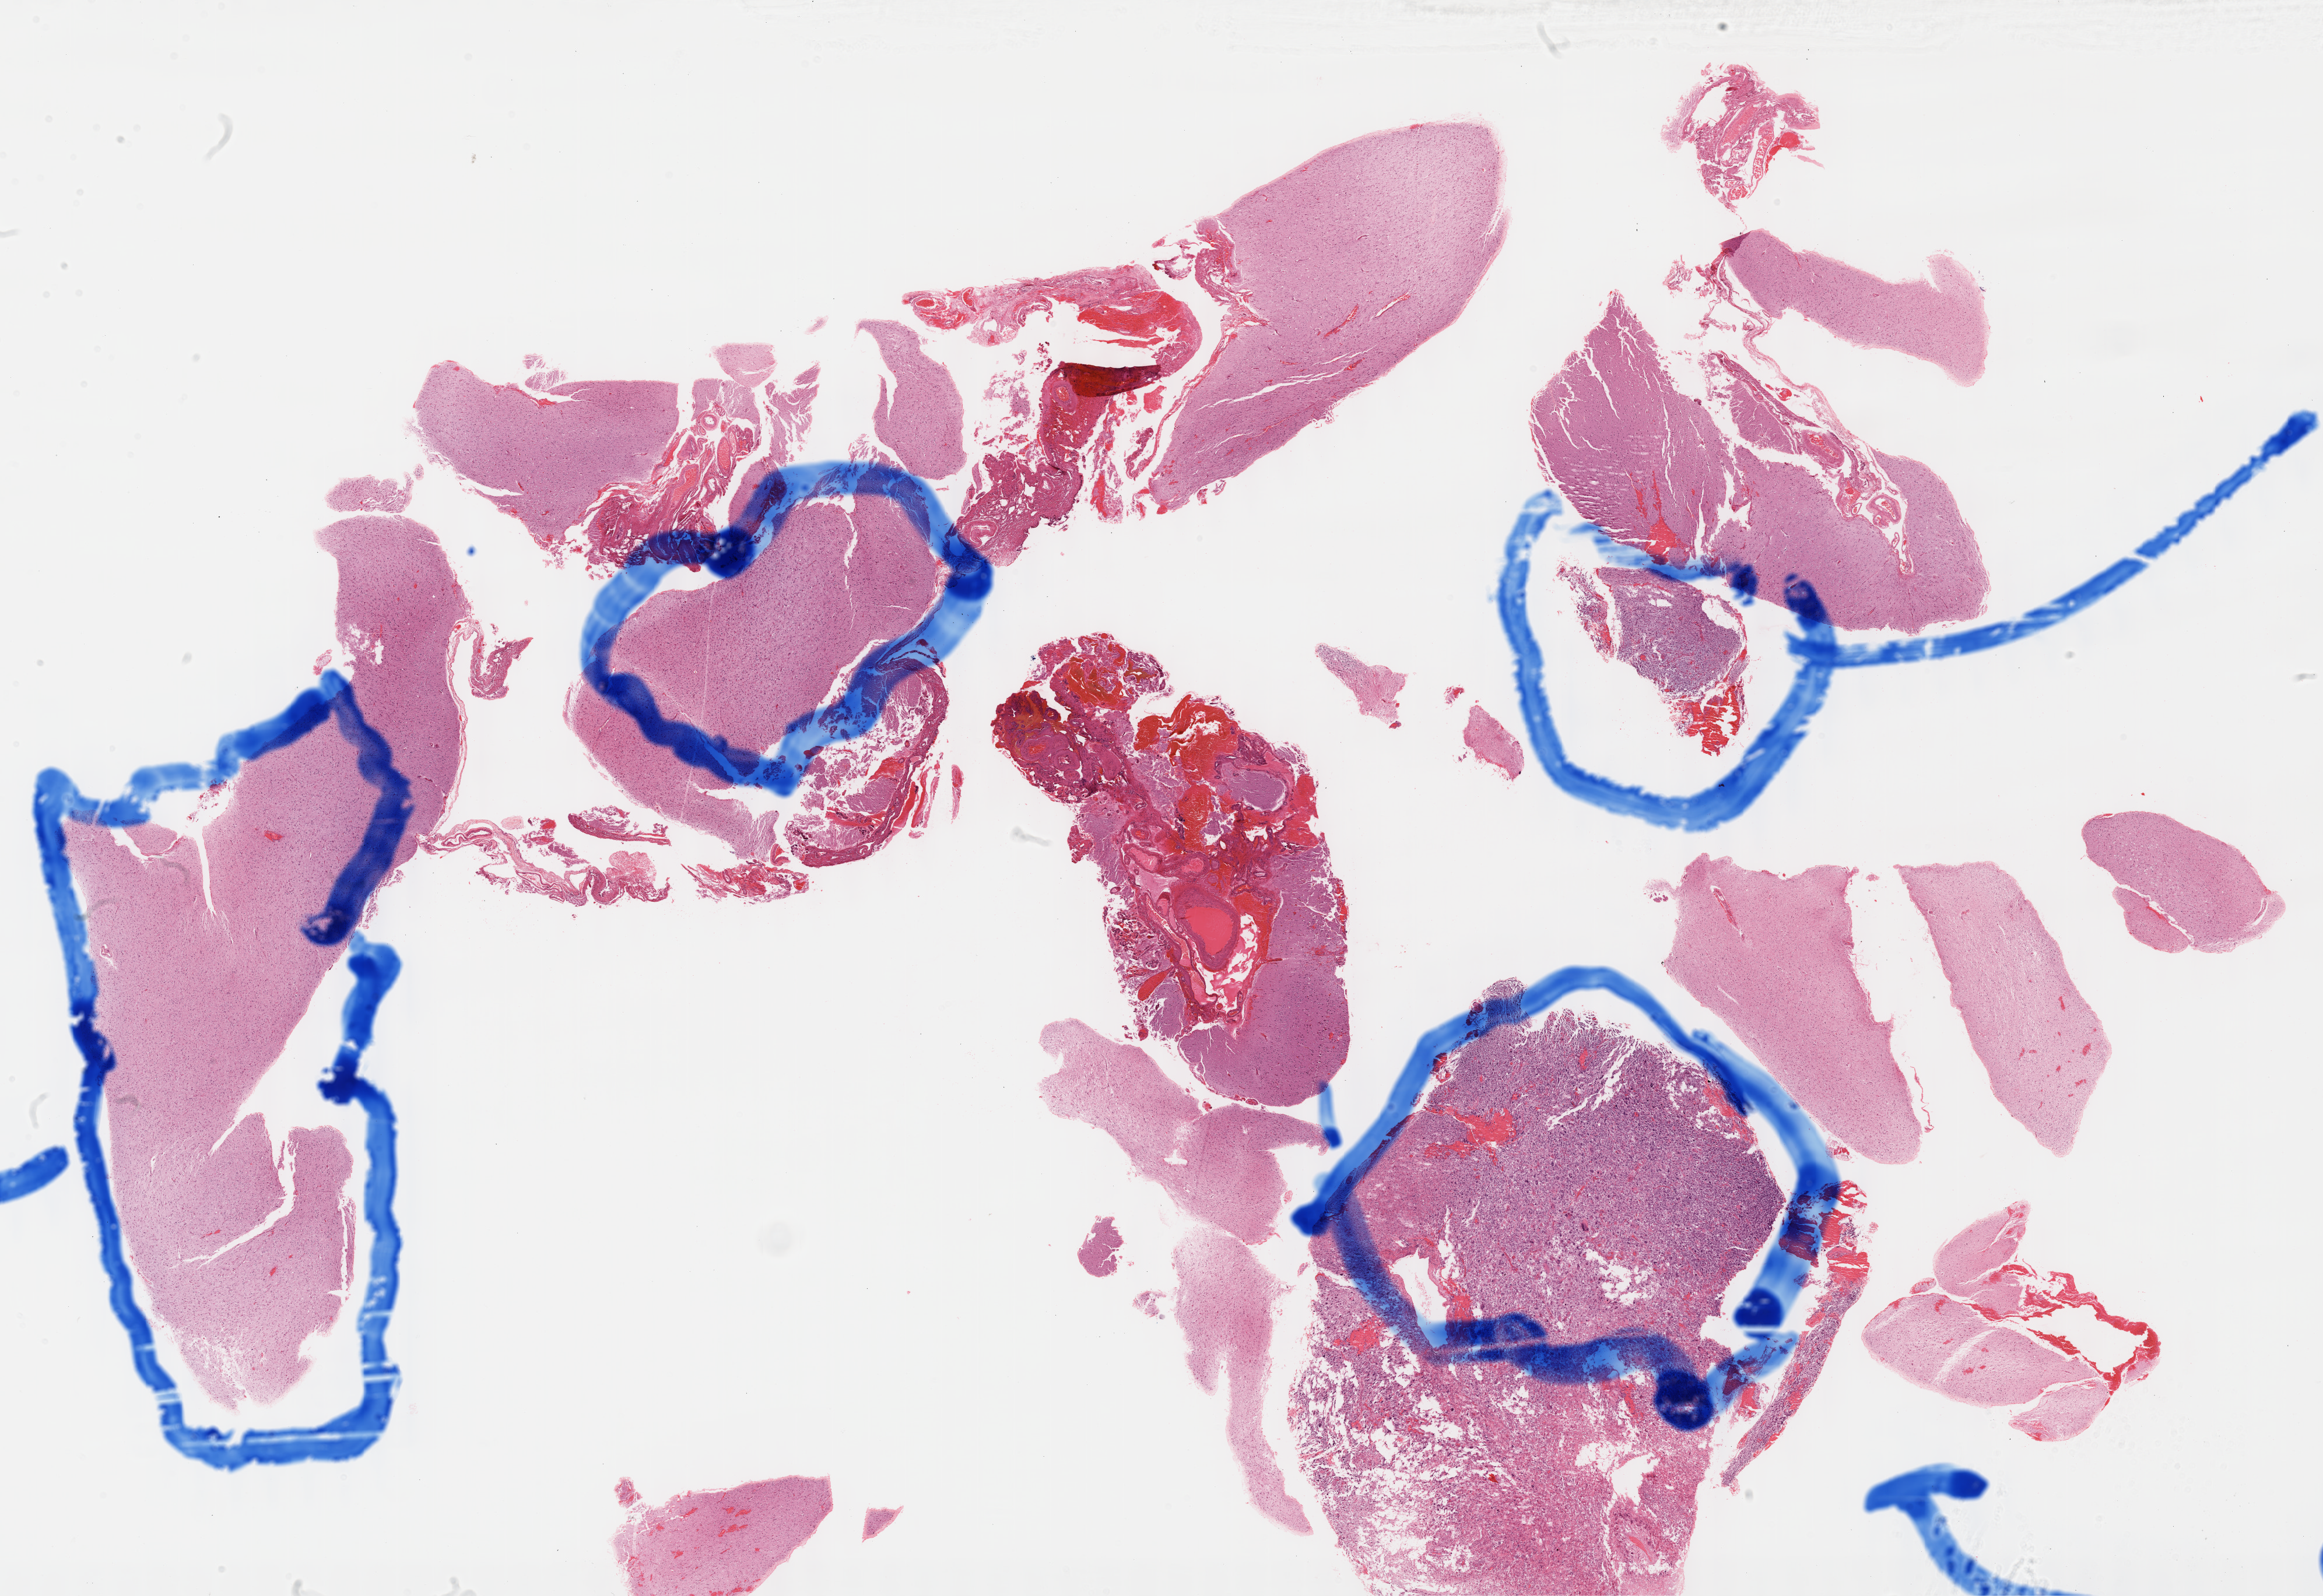
Whole-slide histology image, Hematoxylin and eosin (H&E) stained, a low-resolution overview of the entire scanned area, about 32.2 x 22.1 mm (from a 40x scan); formalin-fixed paraffin-embedded (FFPE) diagnostic section; primary tumour sample from the brain. Patient: male, age at initial diagnosis 32 years.
Diagnosis: Glioblastoma.